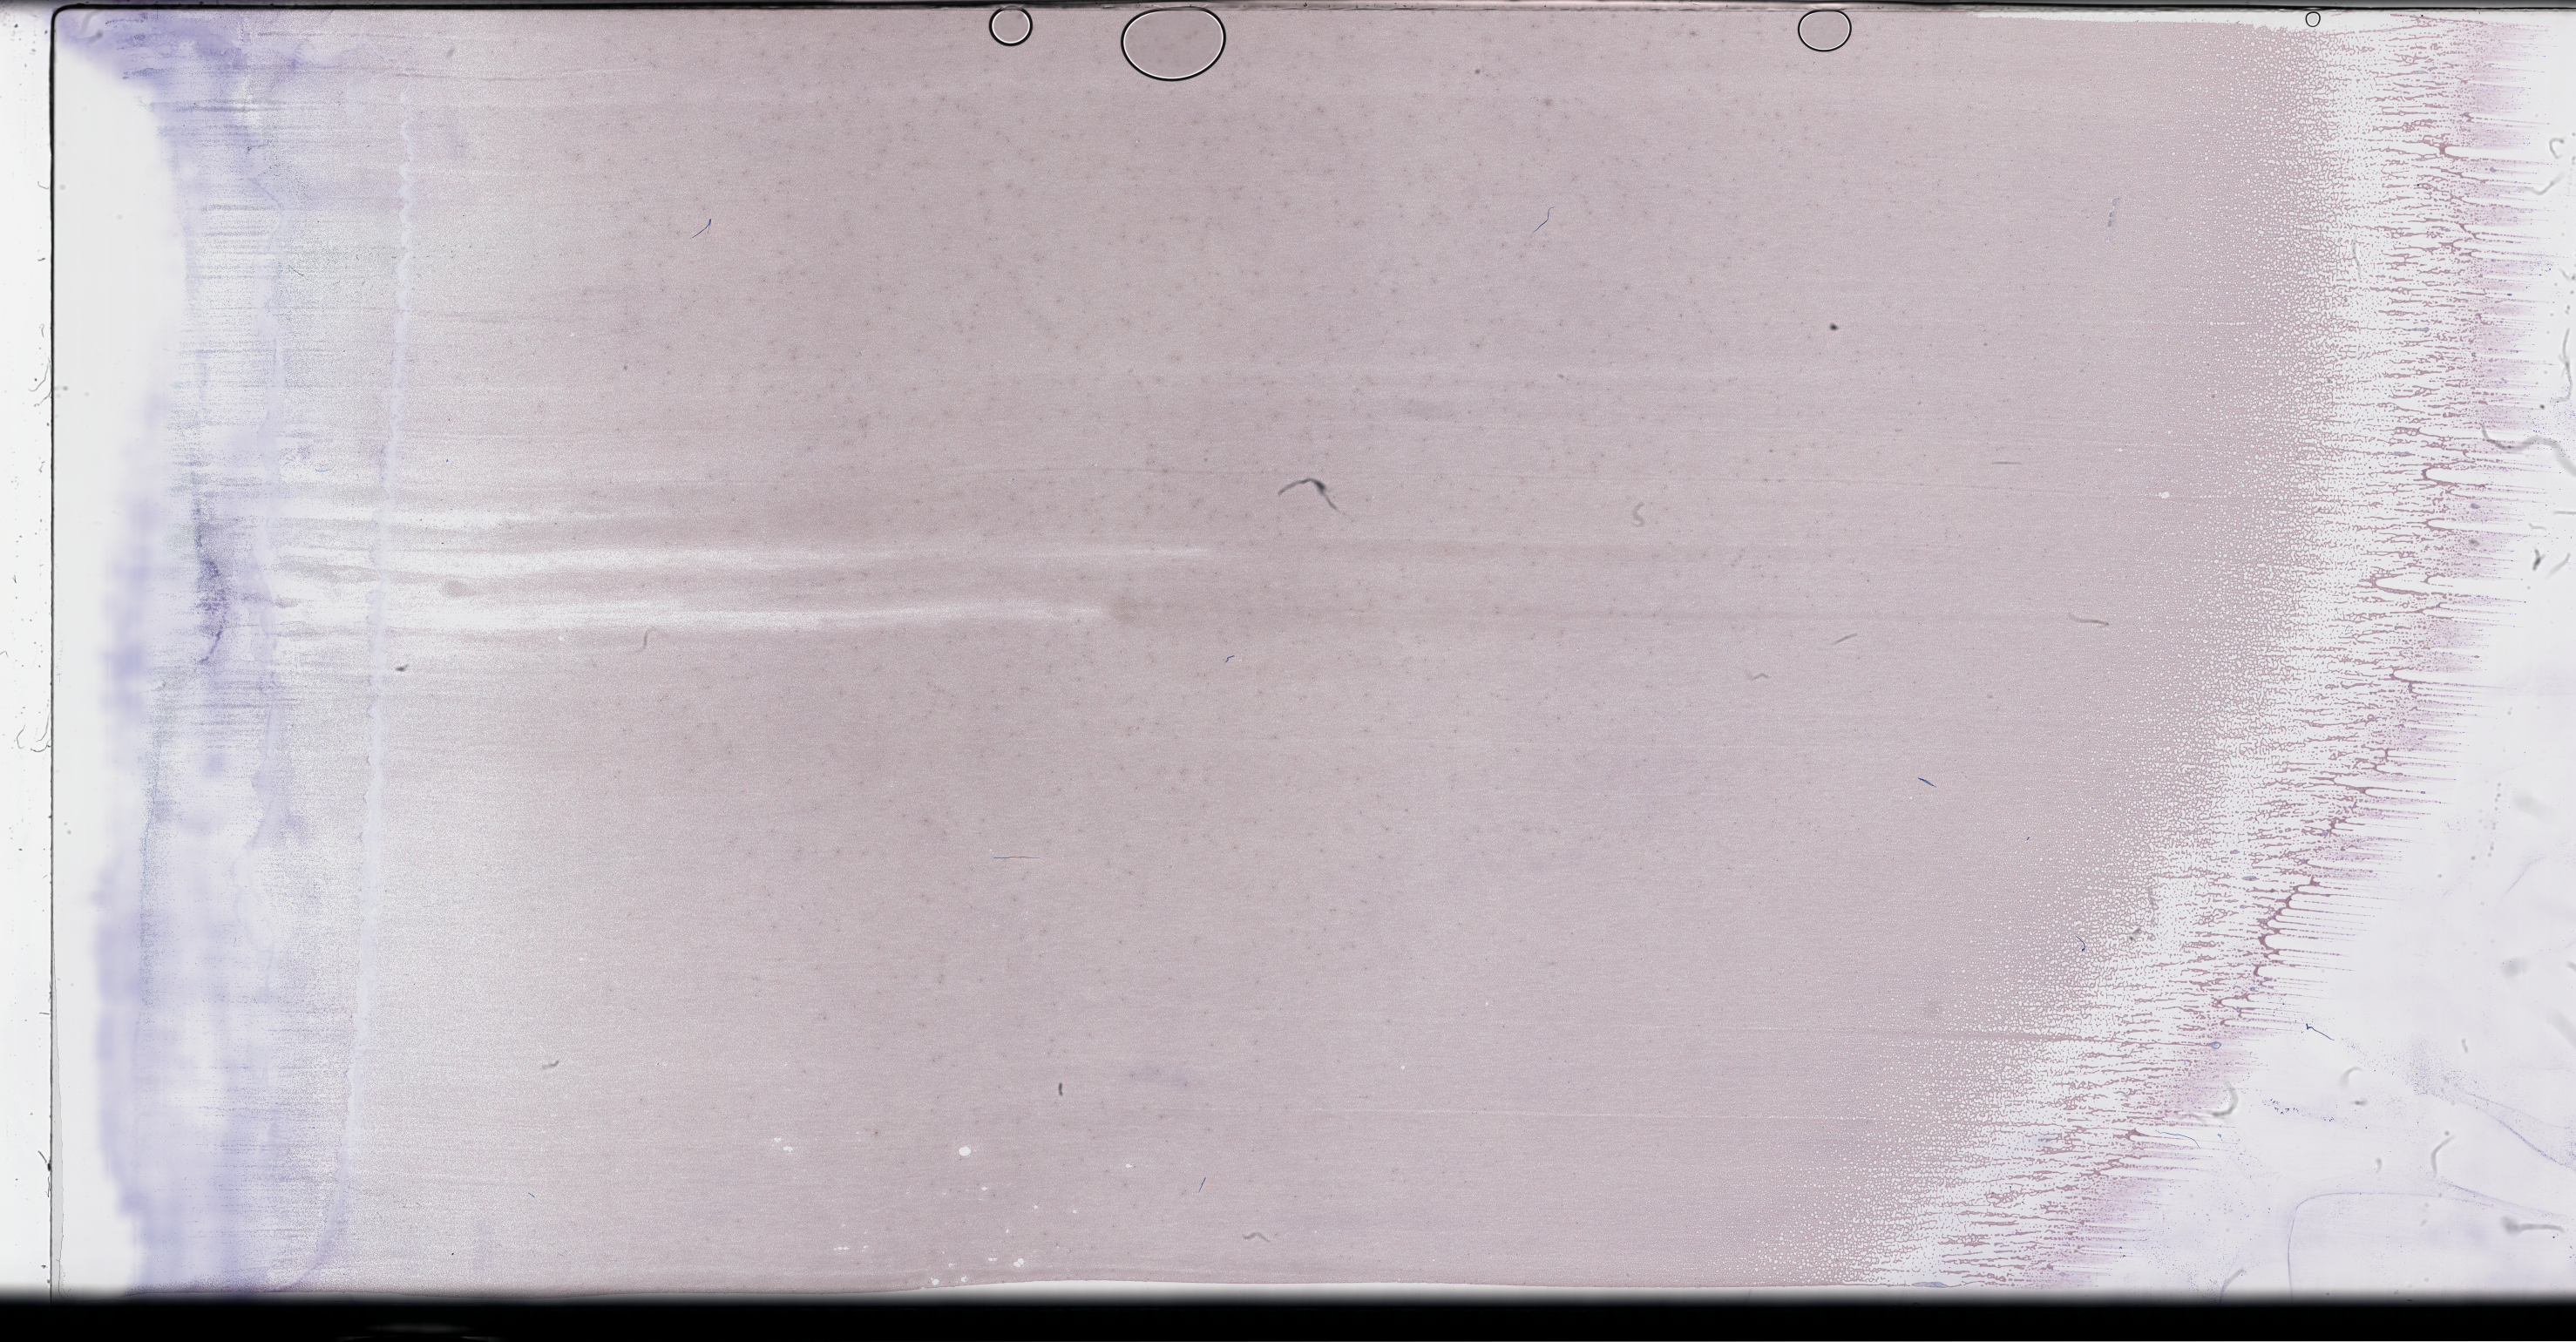
Wright–Giemsa-stained whole blood smear, whole-slide image, shown as a low-resolution overview of the whole scanned area (about 47.7 x 24.9 mm); collected on treatment. Male patient.
- patient diagnosis: Plasma Cell Myeloma